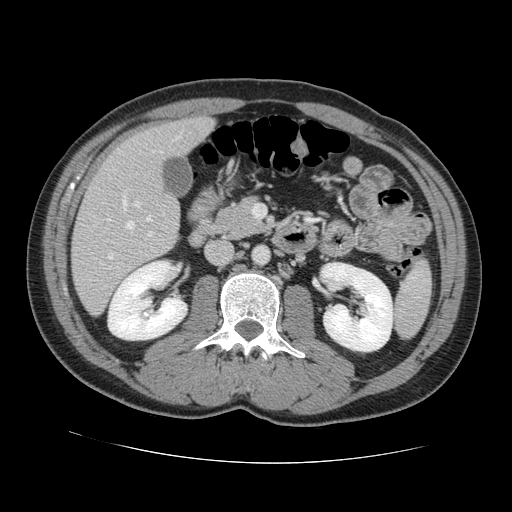
Contrast-enhanced abdominal CT, one axial slice; slice 56 of 131 in the series (ordered by position); 120 kVp; intravenous contrast given; soft-tissue window (W 400 / L 40 HU); 2.5 mm slice thickness; 512 × 512 image matrix, field of view 380 × 380 mm. Male patient, age 40 years. From the clinical record (not read from this slice): diagnosis: colorectal cancer liver metastases, imaged before liver resection; multiple liver metastases: yes; largest metastasis: 2.9 cm; disease in both lobes: yes.
Structures marked on this image (manually delineated by an expert):
- hepatic veins: bounding box [x1, y1, x2, y2] px = [108, 136, 180, 259]
- liver: [73, 118, 213, 313]
- planned liver remnant (the part of the liver to remain after resection): [114, 118, 213, 173]
- portal vein (with intrahepatic branches): [135, 201, 152, 236]